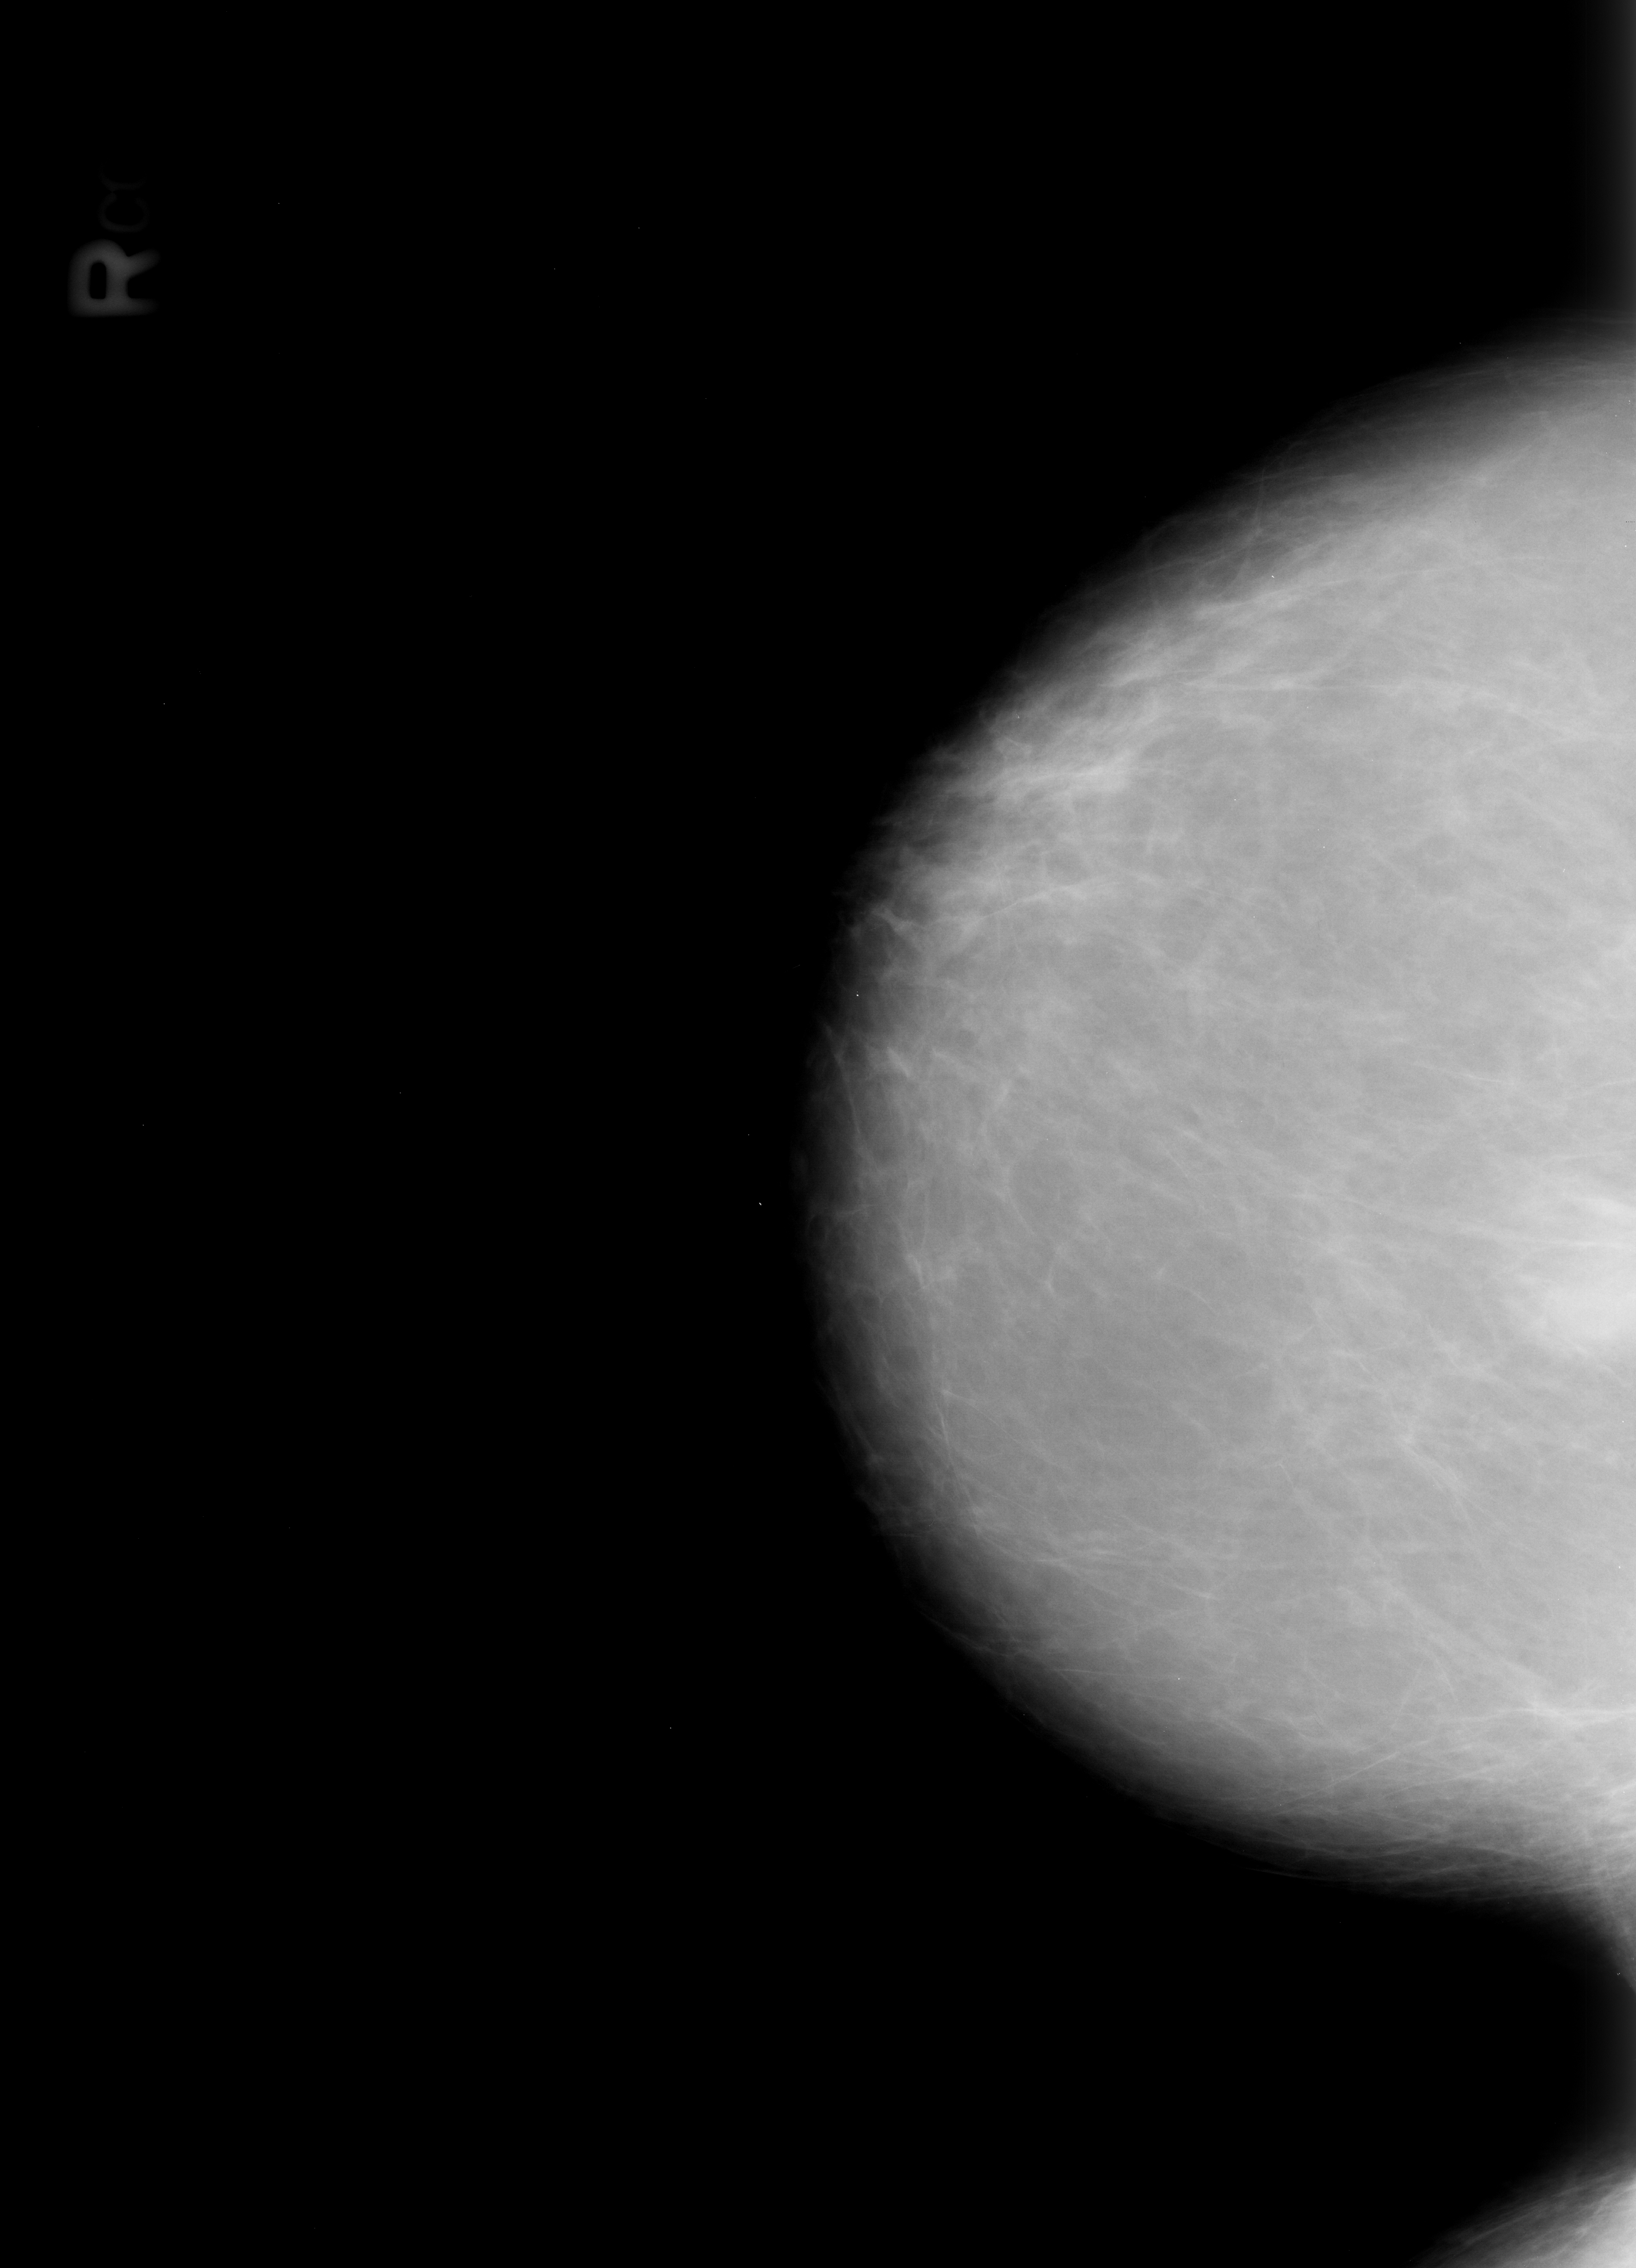
Digitized screen-film mammogram, right breast, CC view, BI-RADS breast density category 2 (scale 1–4).
Abnormality record for this image: mass, shape asymmetric breast tissue; BI-RADS assessment category 2; benign without callback (not worked up further).